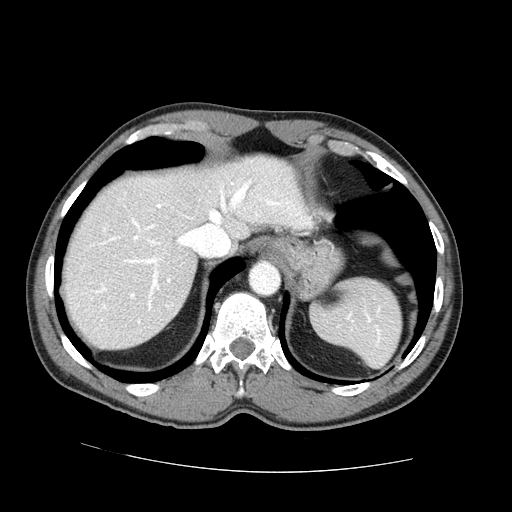
Contrast-enhanced abdominal CT (liver protocol), one axial slice; slice 58 of 73 in the series (ordered by position); reconstruction kernel STANDARD; 100 kVp; one of 2 acquisitions stored at this slice position; soft-tissue window (W 400 / L 40 HU); 512 × 512 image matrix, field of view 380 × 380 mm. From the clinical record (not read from this slice): diagnosis: hepatocellular carcinoma (patient treated with transarterial chemoembolisation; whether this scan precedes or follows treatment is not stated here); TNM stage (as recorded): Stage-IVA; Child-Pugh class: A; tumour differentiation: no biopsy; tumour nodularity: uninodular.
Structures marked on this image (semi-automatic segmentation, software-assisted and operator-edited):
- abdominal aorta: bounding box <250,262,280,295> (left, top, right, bottom; pixels)
- liver parenchyma outside the tumour (the mass and vessels are separate outlines, so this box may not span the whole liver): <64,156,312,348>
- liver vessels: <96,180,309,310>